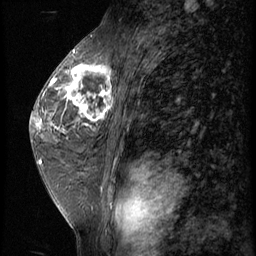
Breast MRI (dynamic contrast-enhanced), one sagittal slice; position 35 of 62 along the scan axis; 3 images stored at this slice position (order not interpretable as contrast timing); 1.5 T; TE 4.2 ms, TR 9 ms; 2.5 mm slice thickness; 256 × 256 image matrix, field of view 180 × 180 mm. Female patient, age 44 years. Case-level facts recorded for this patient, not image findings: setting: breast cancer imaged before/during neoadjuvant chemotherapy; receptor status: triple-negative.
Annotated regions visible in this slice (semi-automatic segmentation, software-assisted and operator-edited):
- analysis volume of interest (the breast-tissue region the enhancement analysis was run in; not a lesion): bounding box [x1, y1, x2, y2] px = [67, 64, 116, 125]
- tumour enhancement mask (voxels above the 140 % enhancement threshold inside the analysis volume of interest): [67, 64, 116, 122]